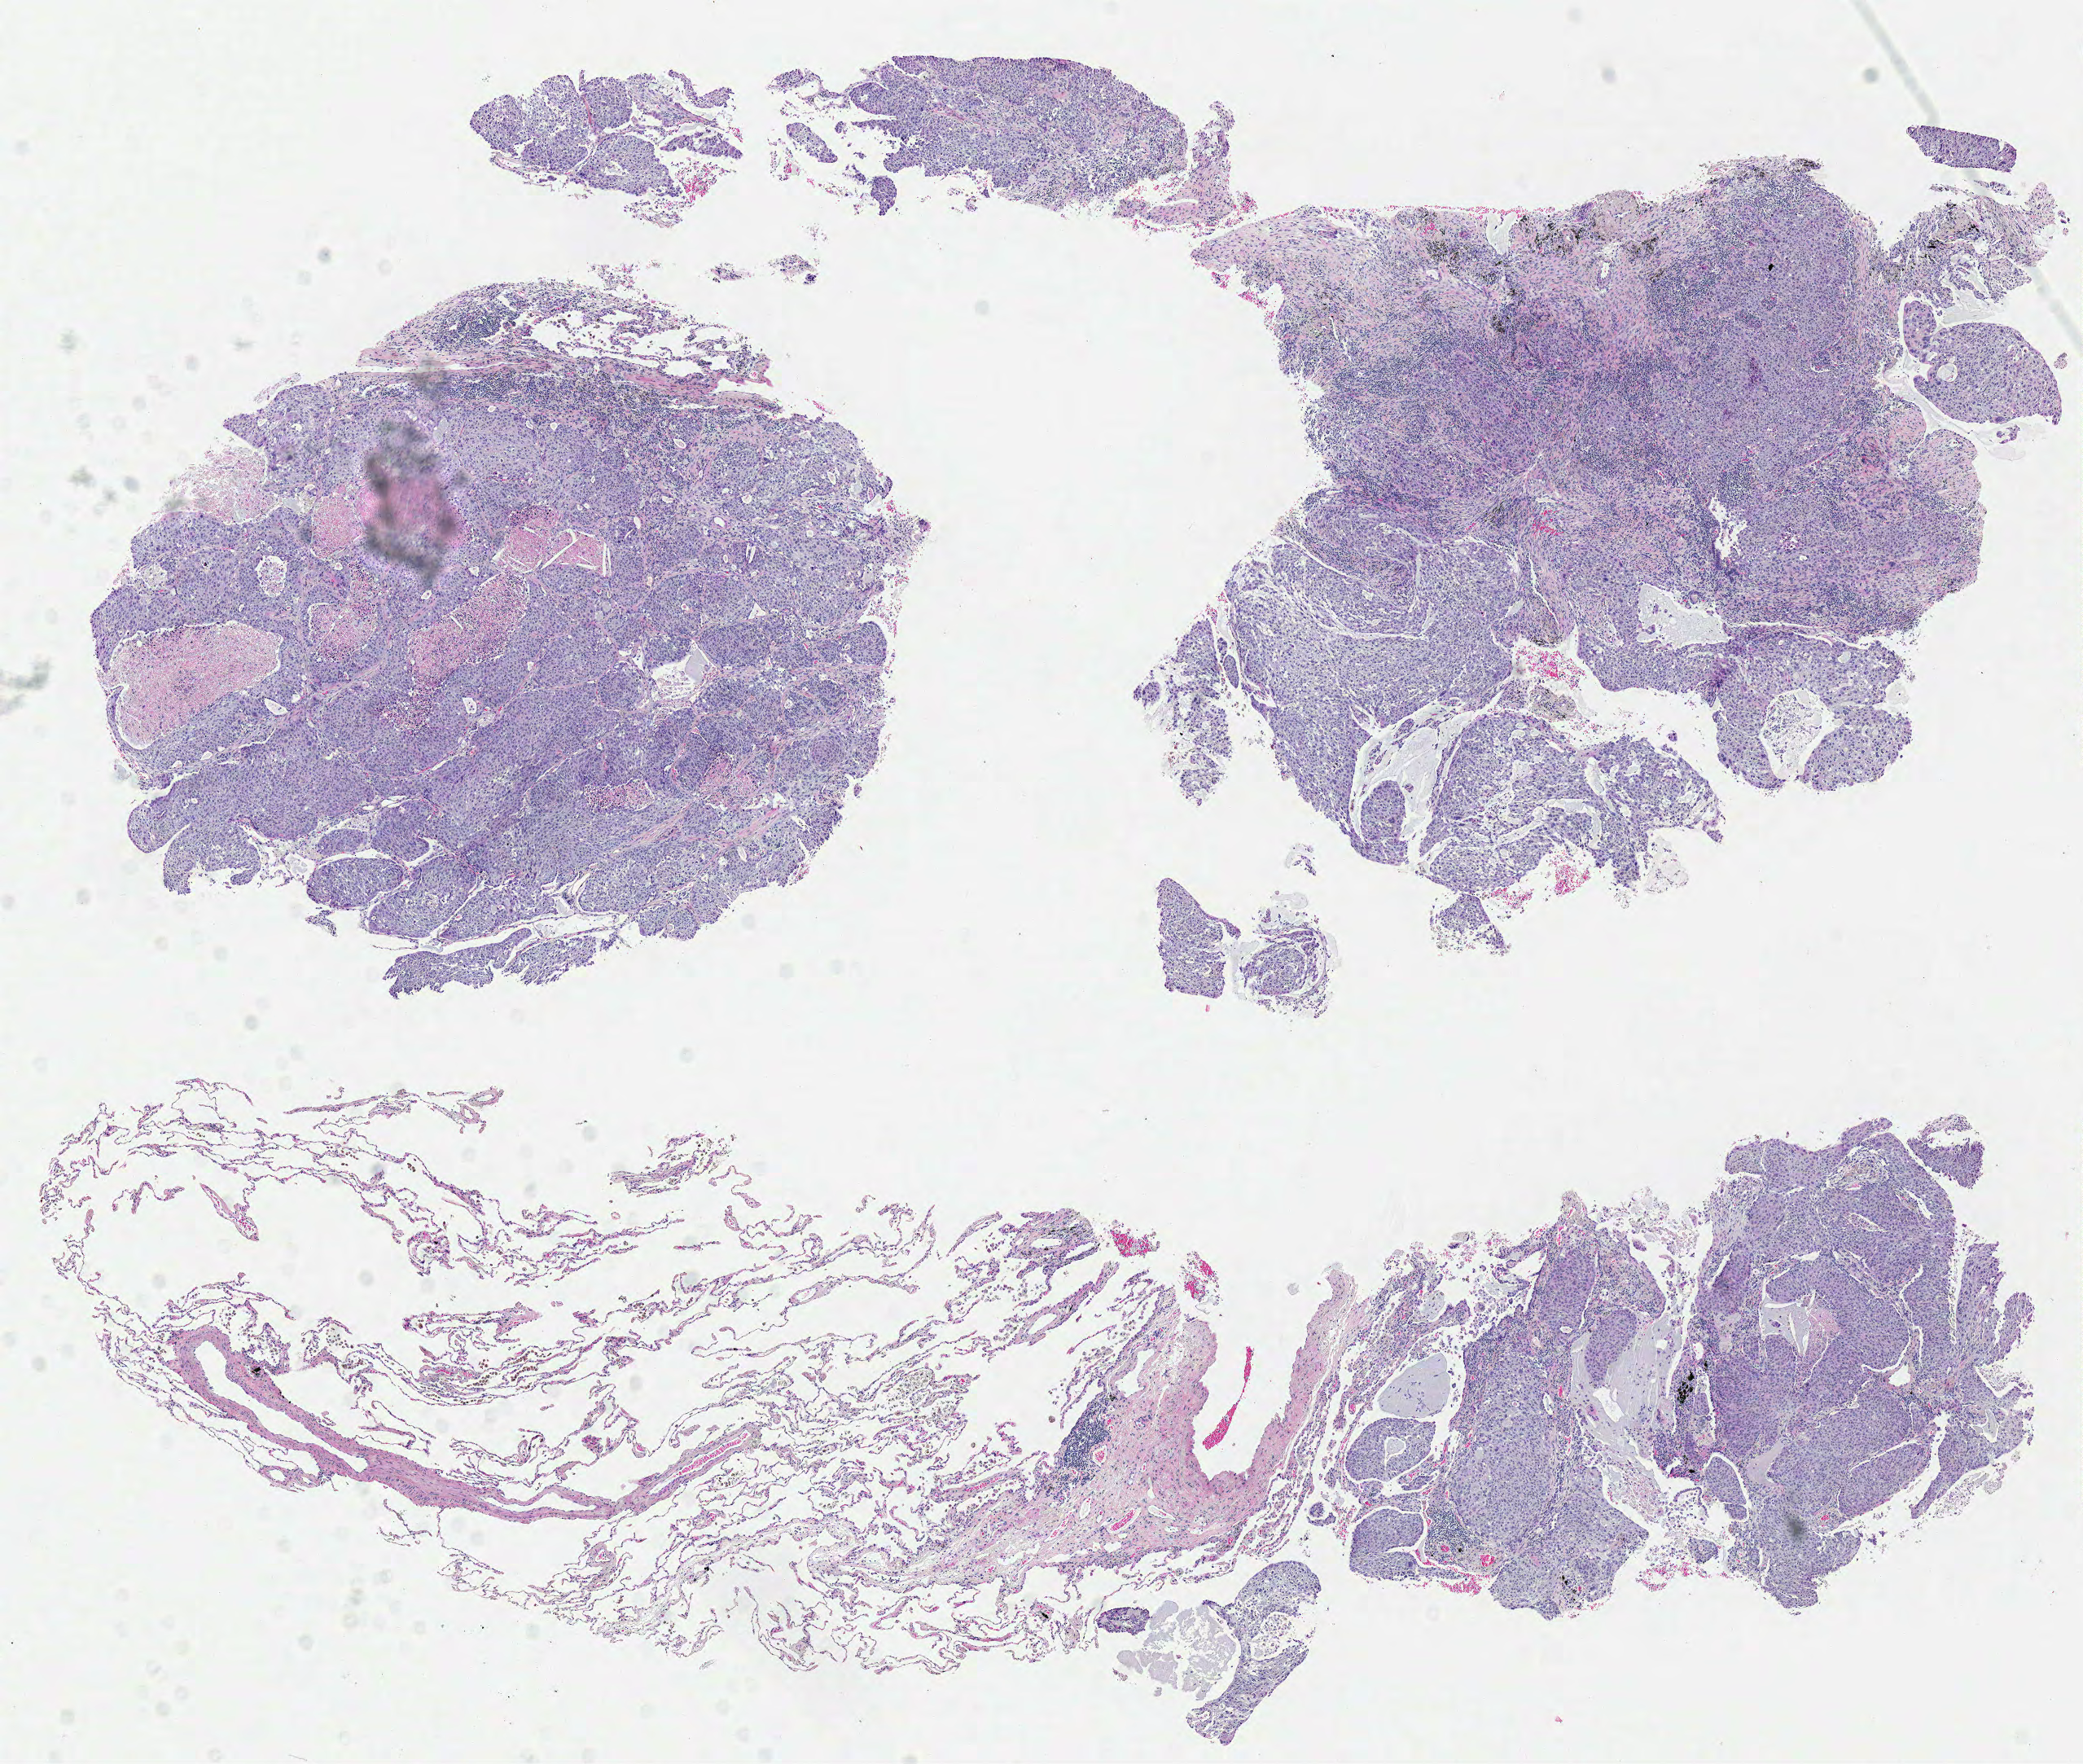
H&E-stained whole-slide image, low-resolution overview of the scanned area, about 10.1 x 8.5 mm. FFPE section. Lung, primary tumour sample. Female patient; age at initial diagnosis 68 years.
Pathologic diagnosis: Squamous cell carcinoma, NOS (upper lobe, lung). TNM: T1 N0 M0. AJCC pathologic stage: IA.